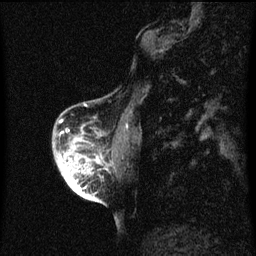
Breast MRI (dynamic contrast-enhanced), one sagittal slice. Dynamic contrast-enhanced series, image 2 of 3 at this slice position (ordered by acquisition). 1.5 T. TE 4.2 ms, TR 8 ms. 256 × 256 image matrix, field of view 180 × 180 mm. Patient: female, 56 years.
Outlined on this slice (semi-automatic segmentation, software-assisted and operator-edited):
- analysis volume of interest (the breast-tissue region the enhancement analysis was run in; not a lesion): bounding box [x1, y1, x2, y2] px = [54, 122, 111, 199]
- tumour enhancement mask (voxels above the 70 % enhancement threshold inside the analysis volume of interest): [60, 138, 100, 199]